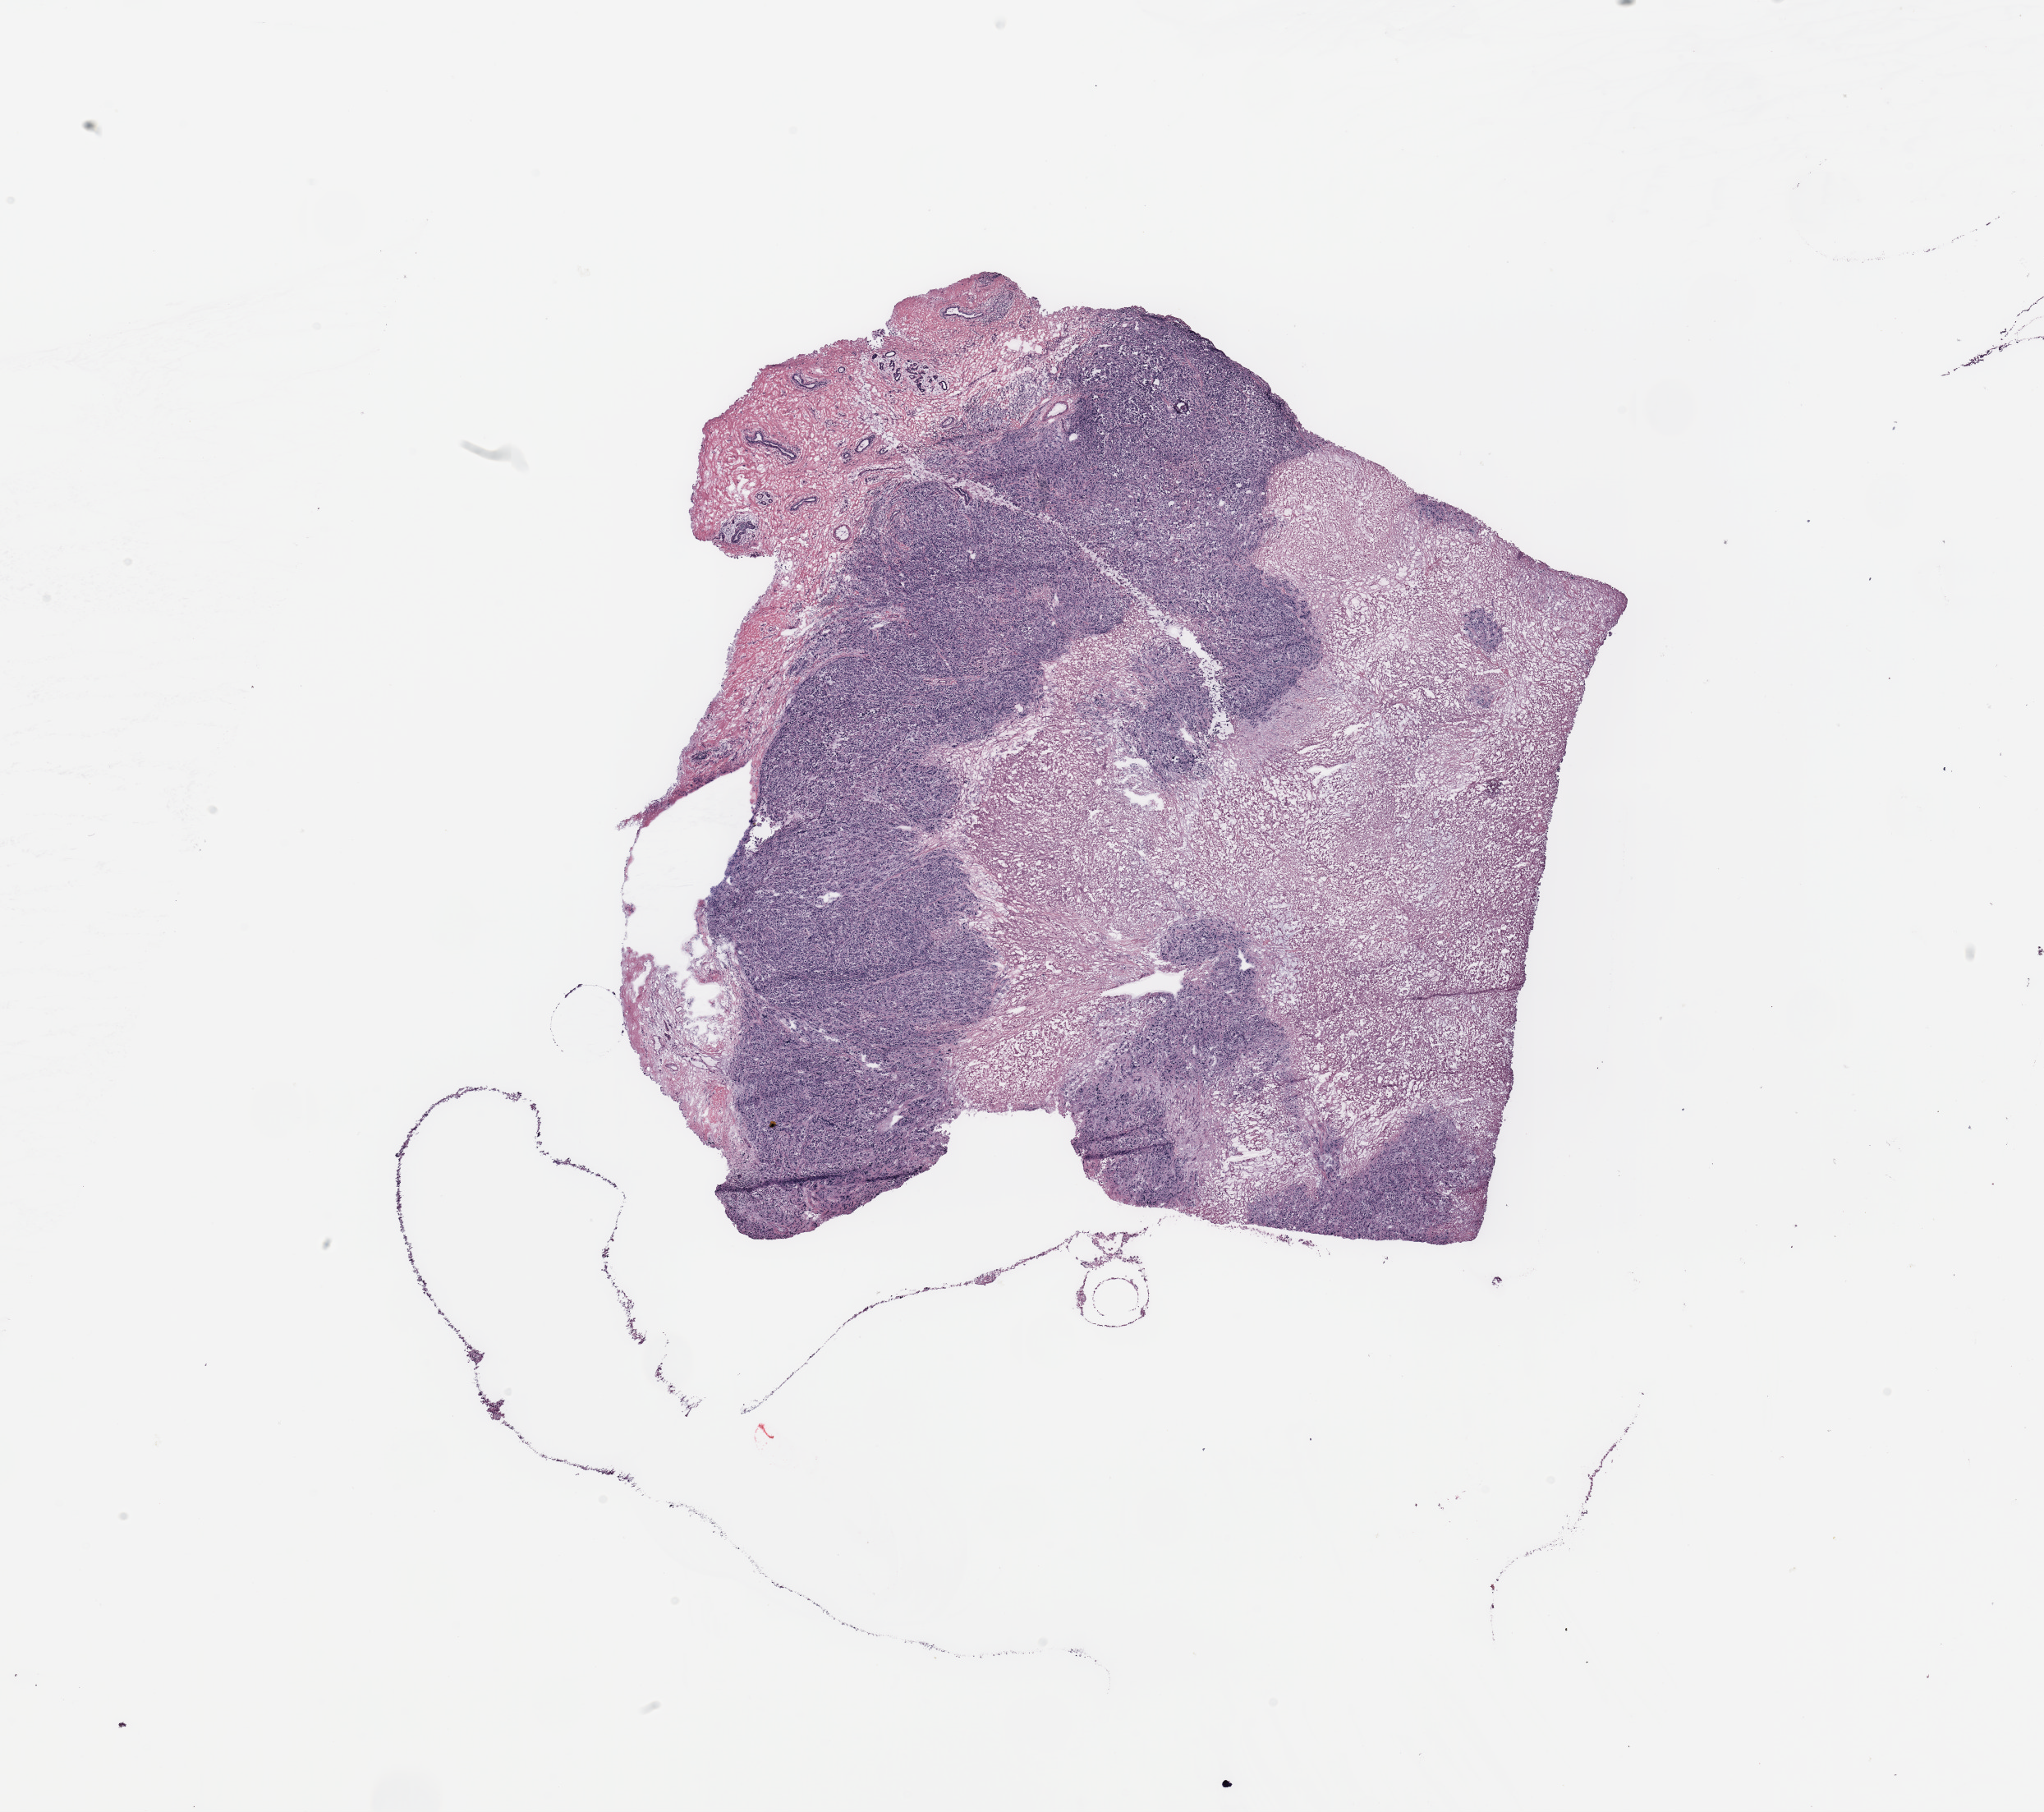
Digitized Hematoxylin and eosin (H&E) stained tissue section (whole slide) — whole scanned area (about 19.7 x 17.4 mm, acquisition: 20x scan) shown as a low-resolution overview, tumour tissue sample, breast. 65-year-old female patient.
Diagnosis: Infiltrating duct carcinoma, NOS.